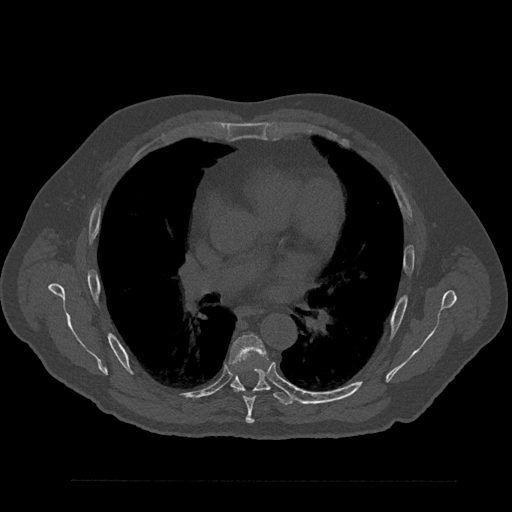
CT including the spine, one axial slice. Position 532 of 797 along the scan axis. Reconstruction kernel Br40s/3. 120 kVp. Bone window (W 1800 / L 400 HU). 0.5 mm slice thickness. 512 × 512 image matrix, field of view 430 × 430 mm. Patient: male, 61 years. Case-level facts recorded for this patient, not image findings: primary cancer: prostate.
Outlined on this slice (semi-automatically segmented with operator editing):
- T6 vertebra: box from (x=230, y=335) to (x=266, y=424) px
- T7 vertebra: (x=230, y=366)–(x=293, y=405)